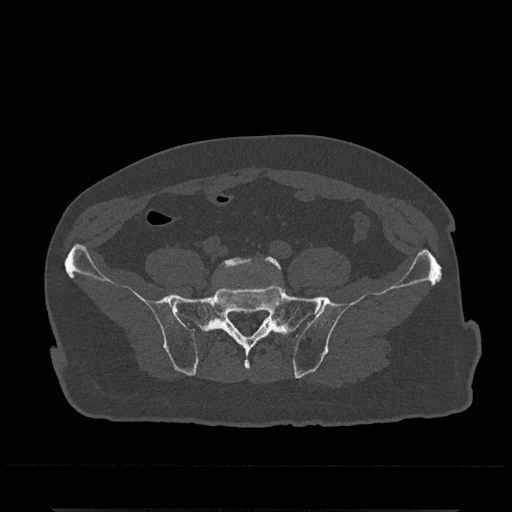
CT including the spine, one axial slice; position 37 of 797 along the scan axis; reconstruction kernel Br40s/3; bone window (W 1800 / L 400 HU); 0.5 mm slice thickness; 512 × 512 image matrix, field of view 393 × 393 mm. Male patient, age 67 years. From the clinical record (not read from this slice): primary cancer: prostate.
Structures marked on this image (semi-automatically segmented with operator editing):
- L5 vertebra: bounding box <218,256,281,277> (left, top, right, bottom; pixels)